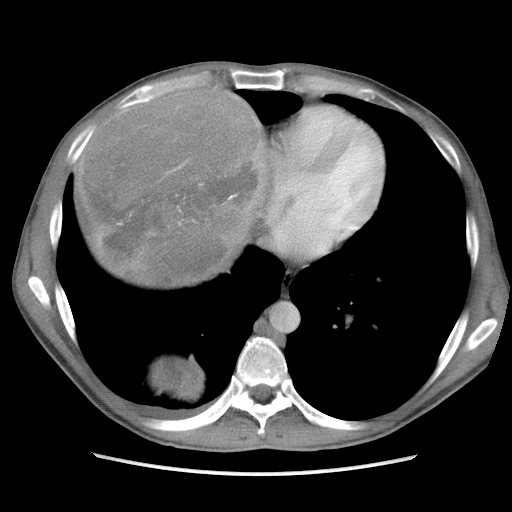
Contrast-enhanced abdominal CT, one axial slice; slice 97 of 115 in the series (ordered by position); soft-tissue window (W 400 / L 40 HU); 512 × 512 image matrix. Male patient. Case-level facts recorded for this patient, not image findings: diagnosis: adrenocortical carcinoma; tumour side: right adrenal; Ki-67 index: 13 %; stage (as recorded): 3.
Structures marked on this image (semi-automatic segmentation, software-assisted and operator-edited):
- mass: bounding box [x1, y1, x2, y2] px = [79, 89, 265, 402]